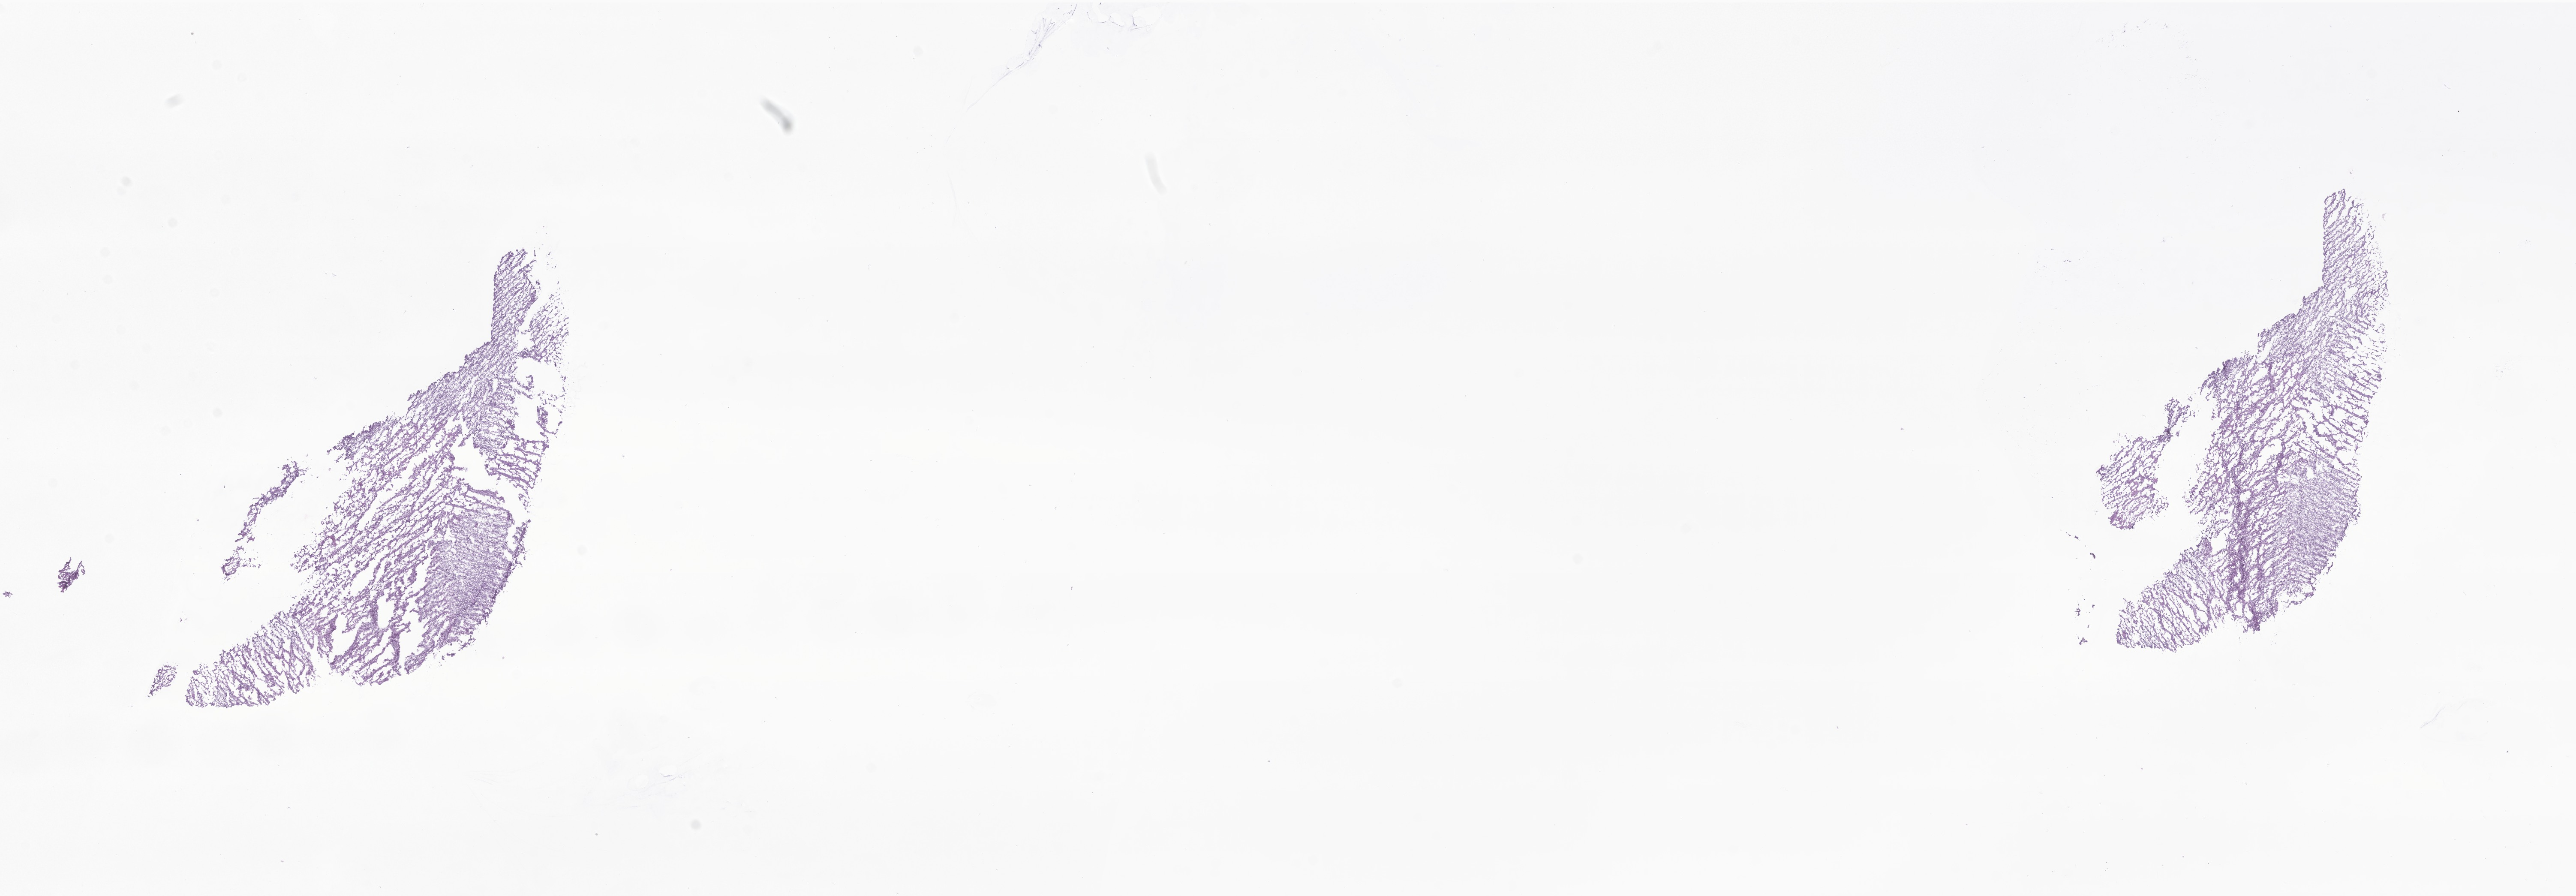
Whole-slide image, H&E stain of tumor tissue from the brain, a low-resolution overview of the entire scanned area, about 25.3 x 8.8 mm; cryosection (OCT / tissue freezing medium). Female patient, age 203 months (16 years 11 months).
Diagnosis: Glioma, malignant.